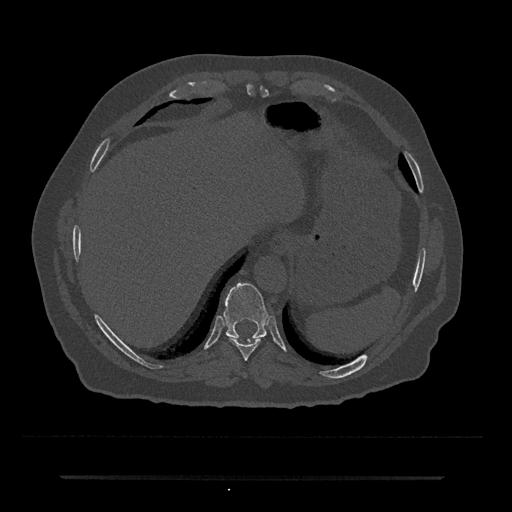
CT including the spine, one axial slice; reconstruction kernel Br40s/3; bone window (W 1800 / L 400 HU); 0.5 mm slice thickness; 512 × 512 image matrix, field of view 437 × 437 mm. Patient: male, 69 years. From the clinical record (not read from this slice): primary cancer: prostate.
Structures marked on this image (semi-automatically segmented with operator editing):
- T10 vertebra: box from (x=223, y=283) to (x=268, y=340) px
- T9 vertebra: (x=229, y=337)–(x=260, y=361)